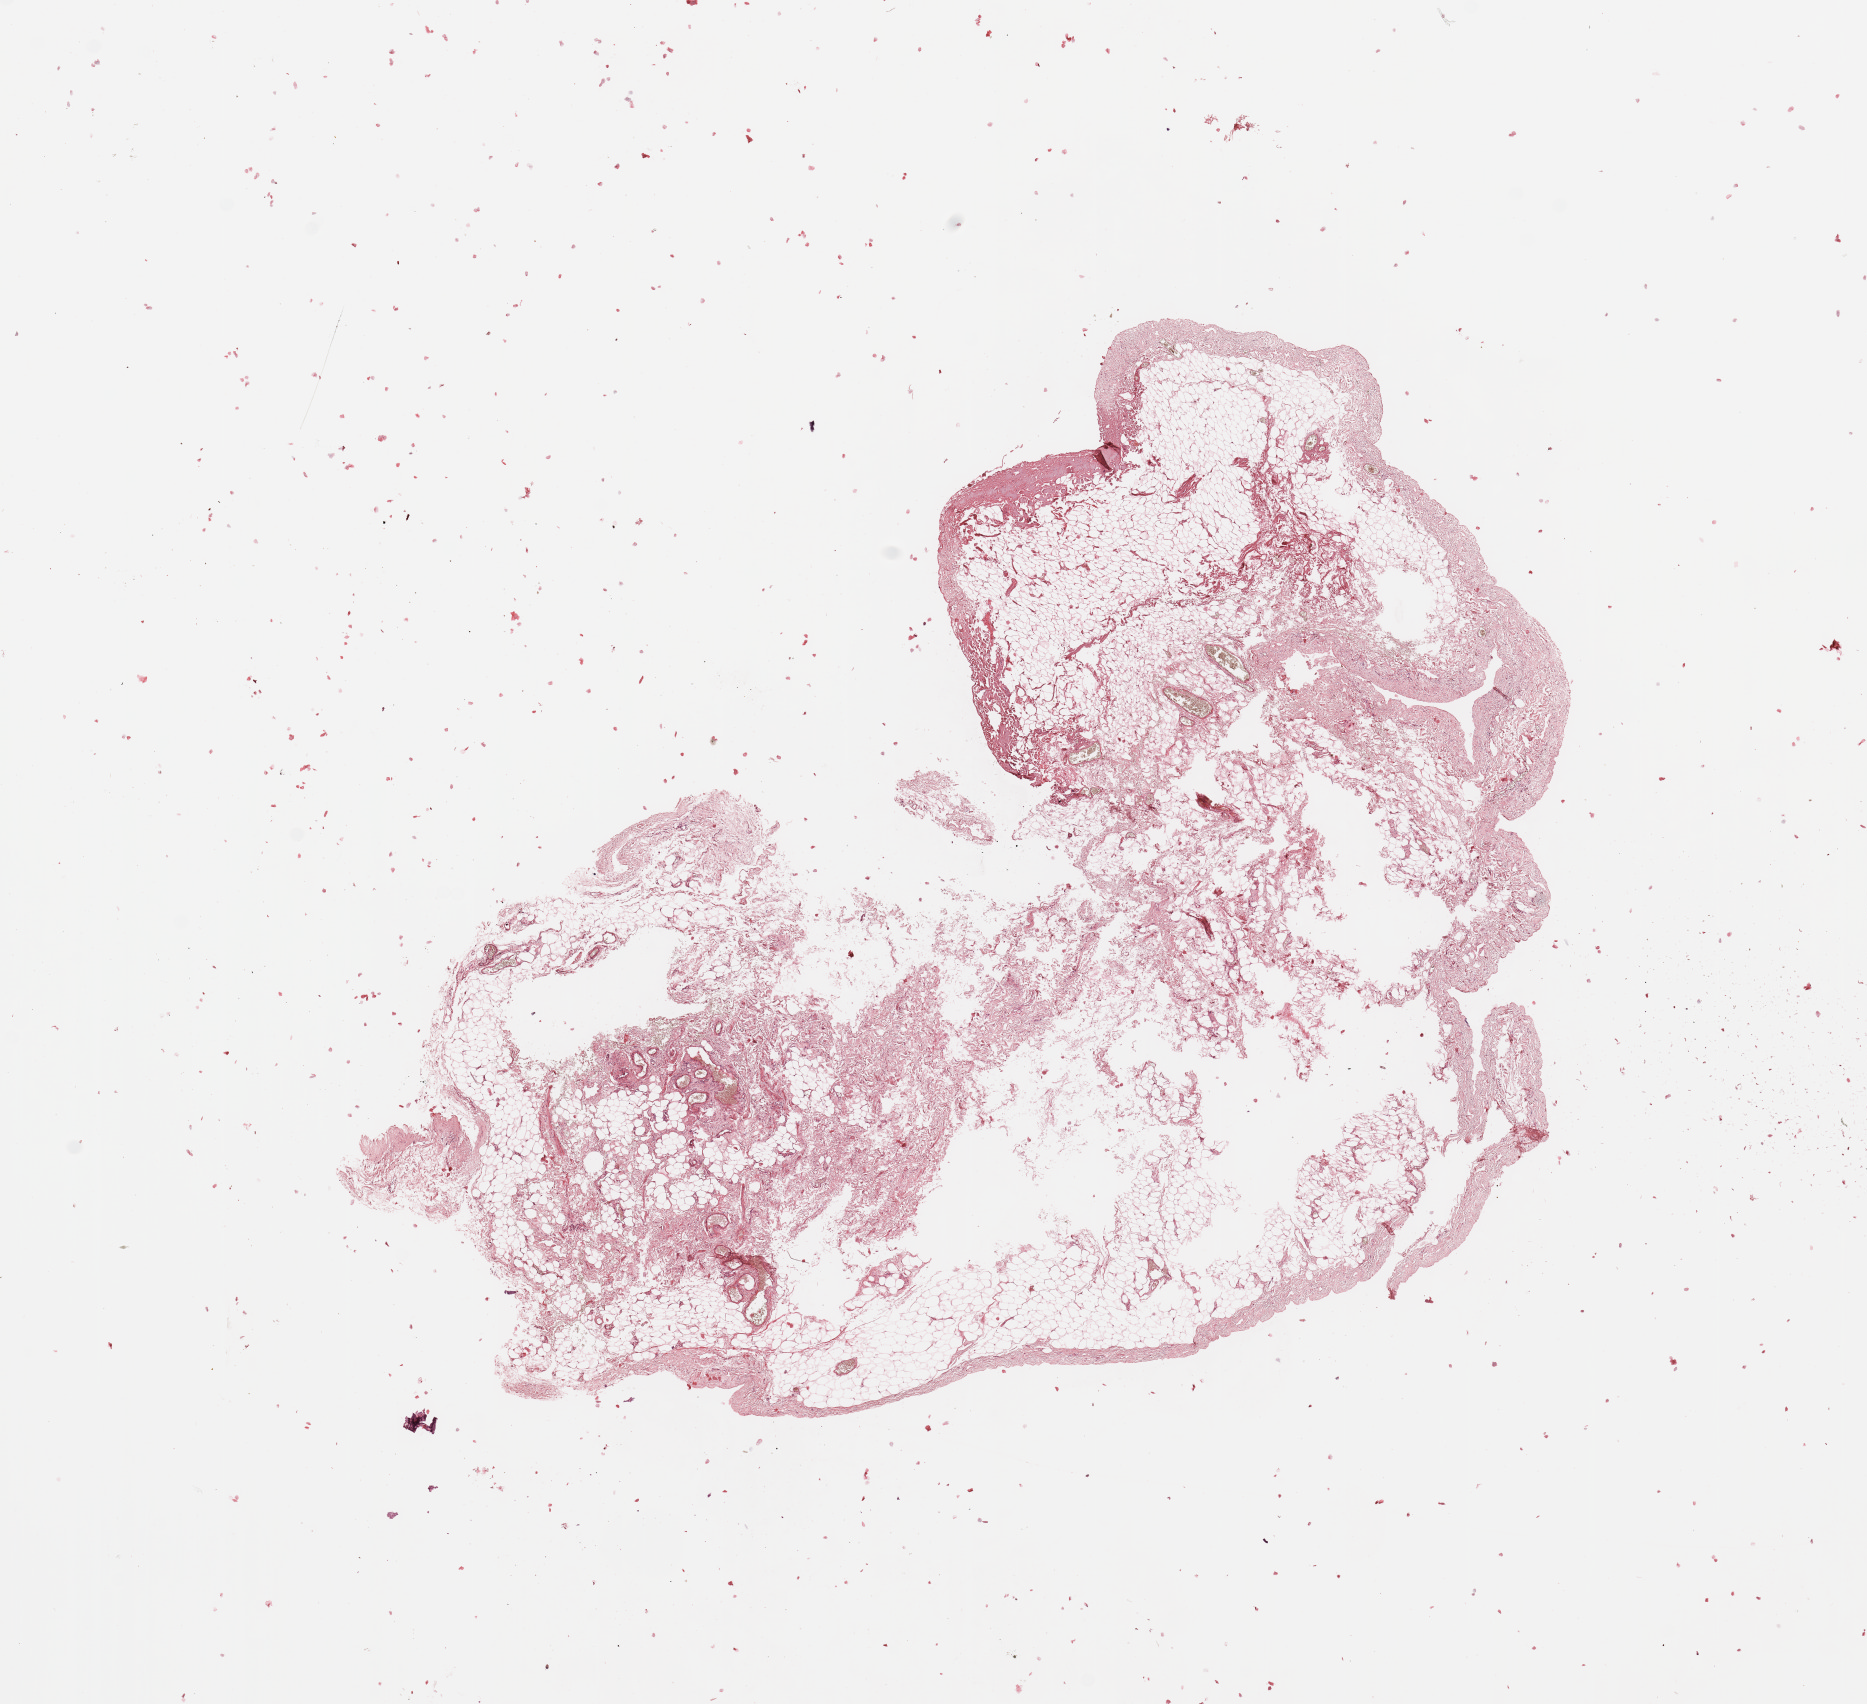
Digitized Hematoxylin and eosin (H&E) stained tissue section (whole slide) — a low-resolution overview of the entire scanned area, about 14.8 x 13.5 mm (from a 20x scan), normal (non-tumour) tissue sample, uterus. Patient: female, age 68 years.
• this section: normal (non-tumour) tissue from the same patient
• patient diagnosis: Endometrioid adenocarcinoma, NOS